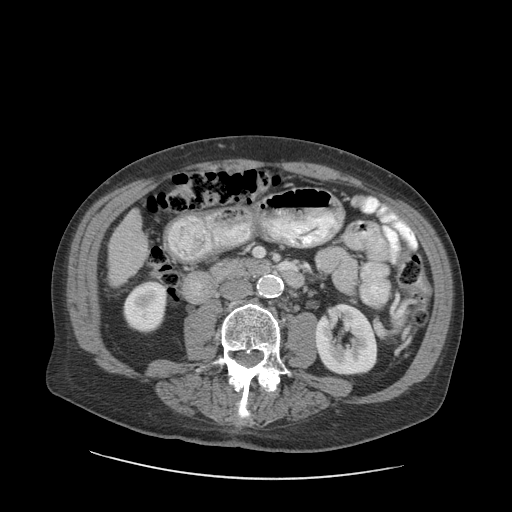
Contrast-enhanced abdominal CT (liver protocol), one axial slice. Position 24 of 89 along the scan axis. Soft-tissue window (W 400 / L 40 HU). 2.5 mm slice thickness. 512 × 512 image matrix, field of view 420 × 420 mm. From the clinical record (not read from this slice): diagnosis: hepatocellular carcinoma (patient treated with transarterial chemoembolisation; whether this scan precedes or follows treatment is not stated here); TNM stage (as recorded): Stage-I; Child-Pugh class: A; tumour differentiation: moderately differentiated; tumour nodularity: uninodular.
Annotated regions visible in this slice (semi-automatic segmentation, software-assisted and operator-edited):
- liver parenchyma outside the tumour (the mass and vessels are separate outlines, so this box may not span the whole liver): box from (x=108, y=209) to (x=148, y=286) px
- liver vessels: (x=140, y=247)–(x=143, y=250)